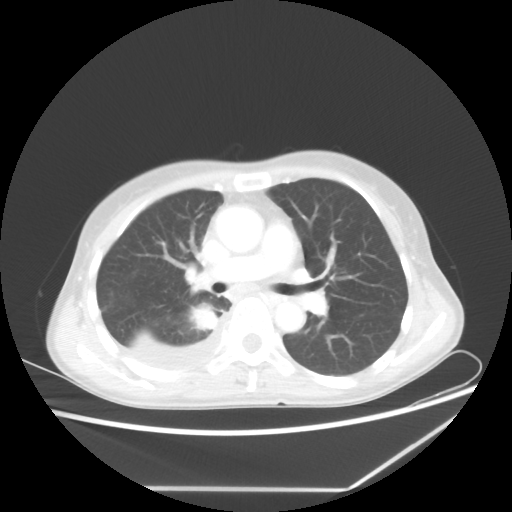
Chest CT, one axial slice; position 36 of 60 along the scan axis; lung window (W 1500 / L -600 HU); 5 mm slice thickness; 512 × 512 image matrix, field of view 364 × 364 mm. Female patient, age 59 years. Case-level facts recorded for this patient, not image findings: clinical TNM (as recorded): T1c N1 M1.
Structures marked on this image (rectangle marked by the reading radiologist):
- lung tumour (recorded histology: adenocarcinoma): bounding box [x1, y1, x2, y2] px = [189, 304, 217, 334]